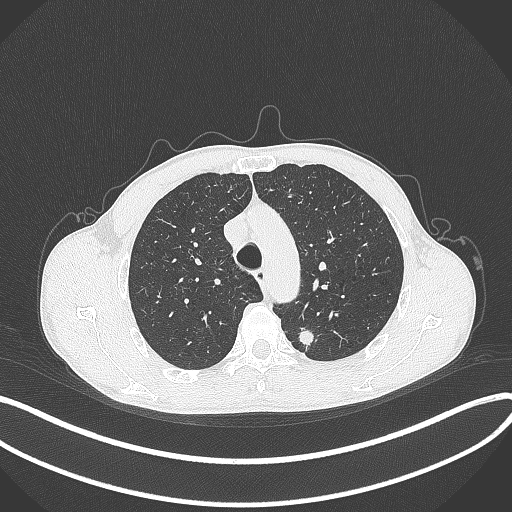
Chest CT, one axial slice; position 300 of 429 along the scan axis; reconstruction kernel B70f; 120 kVp; lung window (W 1500 / L -600 HU); 1 mm slice thickness; 512 × 512 image matrix, field of view 400 × 400 mm. Male patient, age 51 years. Case-level facts recorded for this patient, not image findings: clinical TNM (as recorded): T2a N1 M1.
Outlined on this slice (rectangle marked by the reading radiologist):
- lung tumour (recorded histology: adenocarcinoma): bounding box [x1, y1, x2, y2] px = [293, 321, 317, 348]